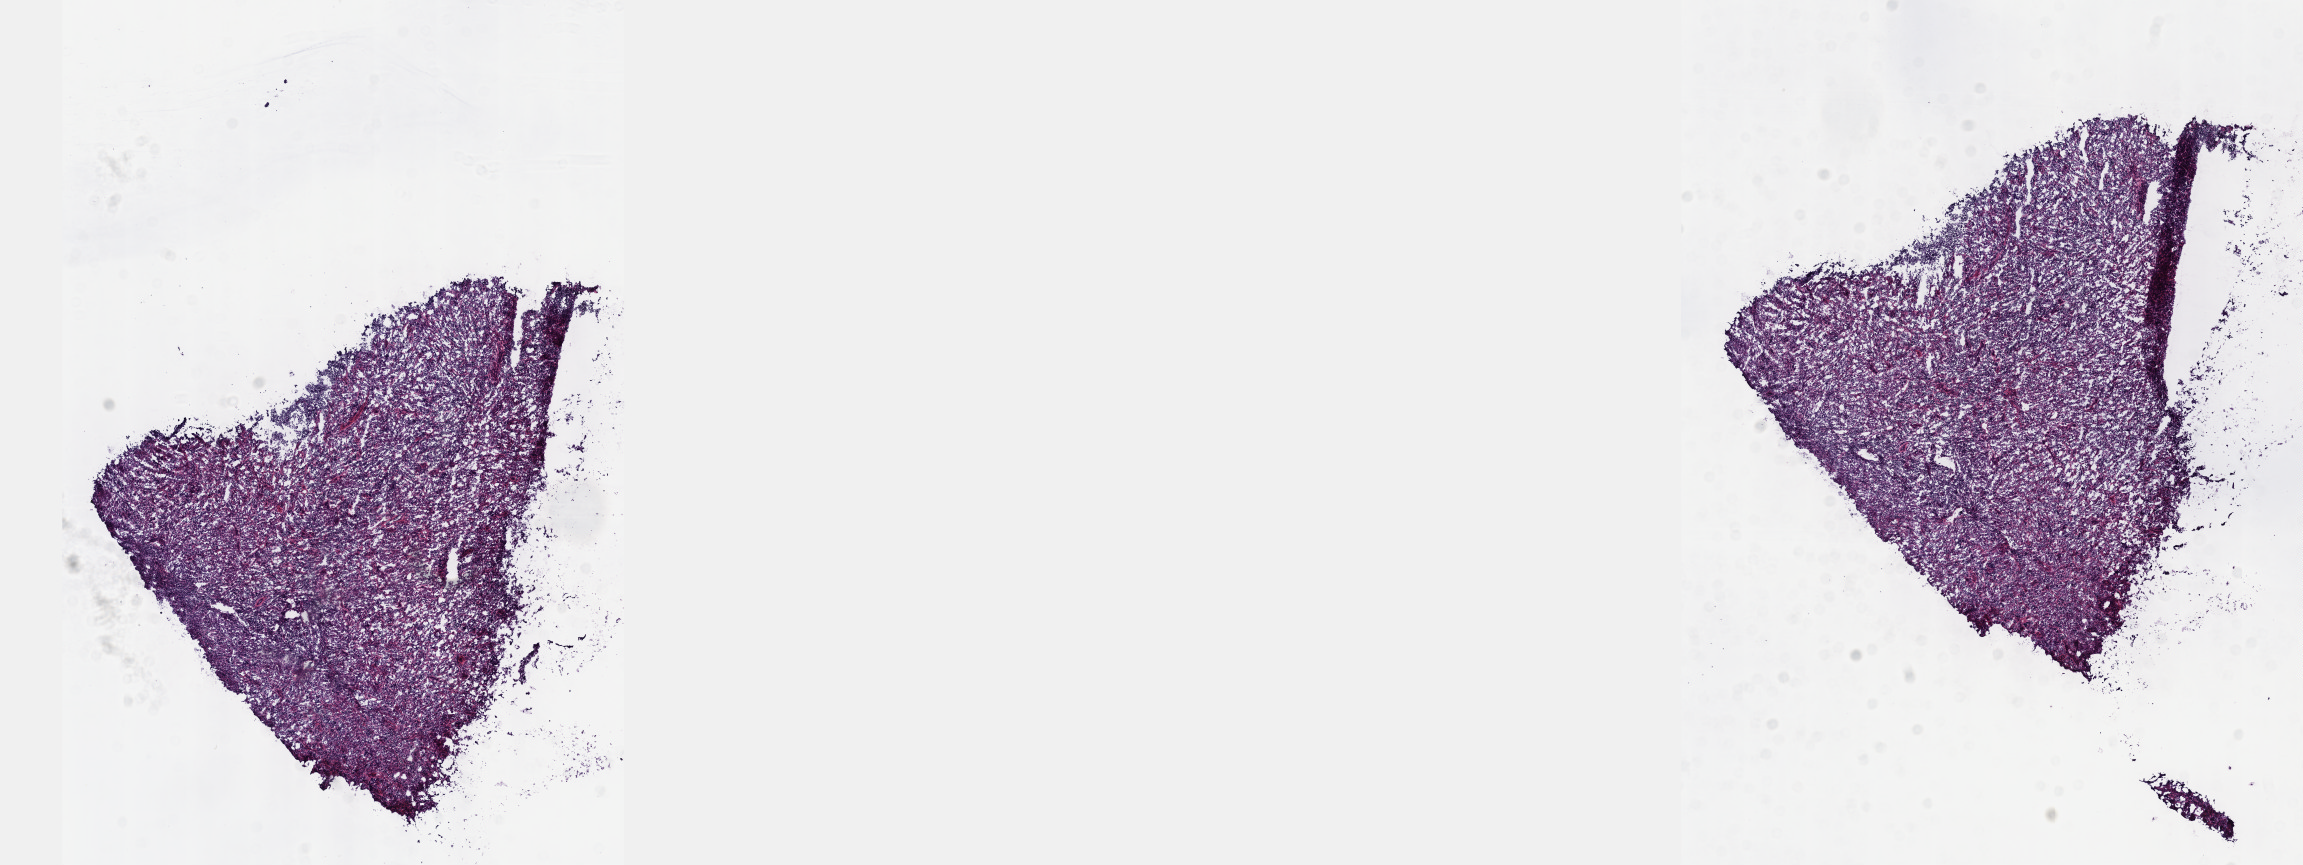
Digitized H&E-stained tissue section (whole slide) — a low-resolution overview of the entire scanned area, about 18.6 x 7.0 mm; frozen section from the top of the tissue portion; primary tumour sample from the testis. Patient: male, age at initial diagnosis 26 years. Composition of this section per pathologist review: tumour cells 90%, tumour nuclei 90%, normal cells 0%, stromal cells 10%, necrosis 0%. Inflammatory infiltration, as recorded: lymphocyte infiltration 40%, monocyte infiltration 20%, neutrophil infiltration 20%.
* laterality: left
* AJCC pathologic stage: IA (7th edition)
* histologic diagnosis: Seminoma, NOS